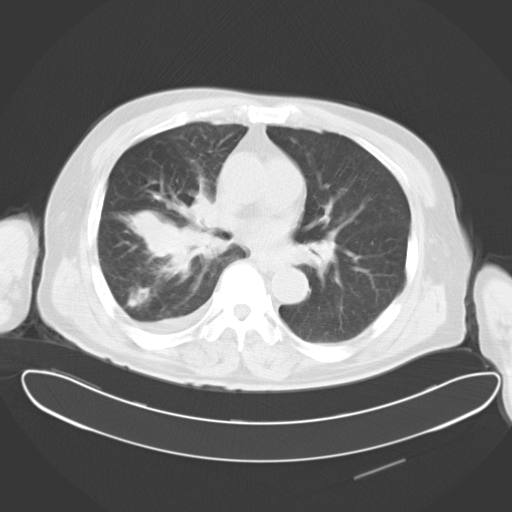
Chest CT, one axial slice. Position 15 of 30 along the scan axis. Reconstruction kernel B40f. 120 kVp. Lung window (W 1500 / L -600 HU). 10 mm slice thickness. 512 × 512 image matrix, field of view 427 × 427 mm. Patient: male, 78 years. Case-level facts recorded for this patient, not image findings: clinical TNM (as recorded): T2 N1 M1.
Annotated regions visible in this slice (rectangle marked by the reading radiologist):
- lung tumour (recorded histology: adenocarcinoma): bounding box (x1, y1, x2, y2) in pixels: (119, 186, 234, 278)